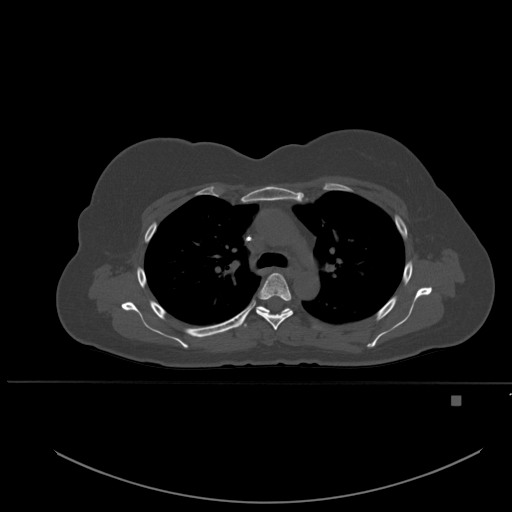
CT including the spine, one axial slice. Bone window (W 1800 / L 400 HU). 512 × 512 image matrix, field of view 443 × 443 mm. Patient: female, 49 years. From the clinical record (not read from this slice): primary cancer: breast.
Outlined on this slice (semi-automatically segmented with operator editing):
- T4 vertebra: bounding box (x1, y1, x2, y2) in pixels: (256, 273, 293, 330)
- T5 vertebra: (242, 306, 292, 328)